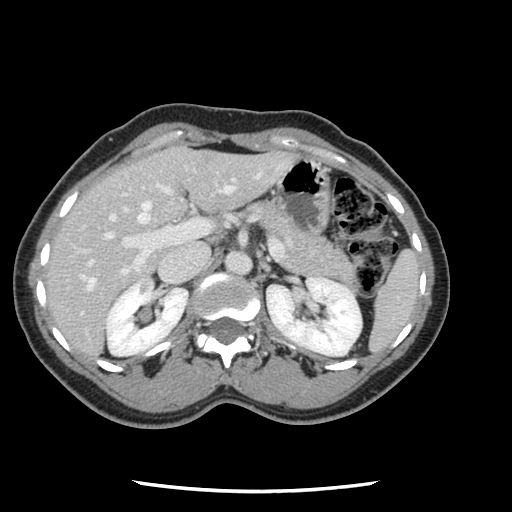
Contrast-enhanced abdominal CT, one axial slice; slice 70 of 134 in the series (ordered by position); 120 kVp; intravenous contrast given; soft-tissue window (W 400 / L 40 HU); 2.5 mm slice thickness; 512 × 512 image matrix, field of view 330 × 330 mm. Female patient, age 43 years. From the clinical record (not read from this slice): diagnosis: colorectal cancer liver metastases, imaged before liver resection; multiple liver metastases: yes; largest metastasis: 3.4 cm; disease in both lobes: yes.
Annotated regions visible in this slice (outlined manually by an expert reader):
- hepatic veins: bounding box (x1, y1, x2, y2) in pixels: (81, 184, 233, 290)
- liver: (47, 147, 294, 357)
- planned liver remnant (the part of the liver to remain after resection): (47, 150, 186, 303)
- portal vein (with intrahepatic branches): (75, 178, 235, 288)